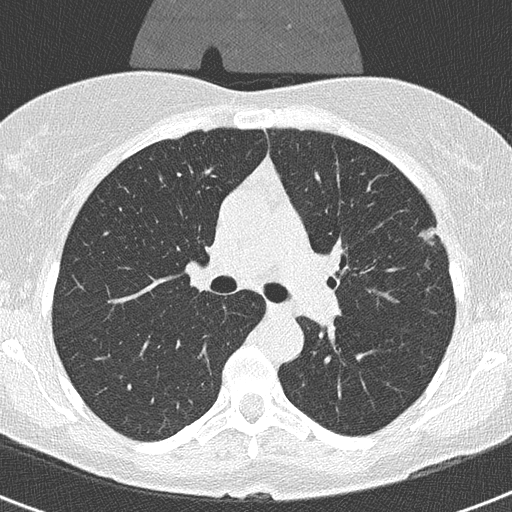
Axial slice from a low-dose chest CT screening exam; second annual screen; lung window (W 1500 / L -600 HU); 2 mm slice thickness; lung (sharp) reconstruction kernel (B50f); 512 × 512 image matrix, field of view 290 × 290 mm. Female participant, aged 56 years at enrolment. Former smoker at enrolment.
Lesion marked by an expert reader, bounding box (x1, y1, x2, y2) in pixels: (403, 201, 454, 256). Reader record for this screening exam (exam-level; its link to the box is not recorded): non-calcified nodule or mass ≥4 mm, left upper lobe, 20 × 9 mm, smooth margins, soft tissue attenuation, pre-existing on the prior screen: yes; interval growth: yes. Official screen result: positive, other. Lung cancer was diagnosed 55 days after this screen: adenocarcinoma, NOS, left upper lobe, moderately differentiated (G2), stage IA (AJCC 6th edition), 11 mm at pathology.